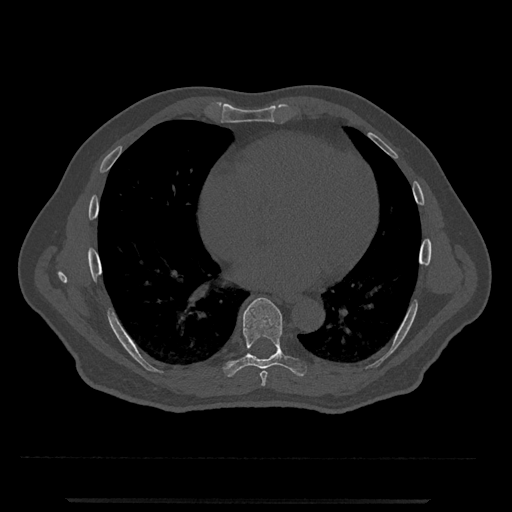
CT including the spine, one axial slice. Position 633 of 797 along the scan axis. Reconstruction kernel Br40s/3. 120 kVp. Bone window (W 1800 / L 400 HU). 512 × 512 image matrix. Male patient, age 63 years. Case-level facts recorded for this patient, not image findings: primary cancer: prostate.
Outlined on this slice (semi-automatically segmented with operator editing):
- T7 vertebra: bounding box (x1, y1, x2, y2) in pixels: (260, 371, 268, 387)
- T8 vertebra: (224, 298, 307, 377)